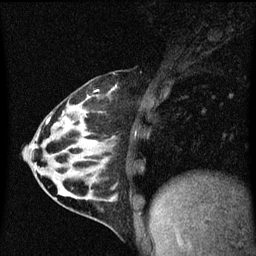
Breast MRI (dynamic contrast-enhanced), one sagittal slice. Dynamic contrast-enhanced series, image 2 of 3 at this slice position (ordered by acquisition). 1.5 T. TE 4.2 ms, TR 8.4 ms. 256 × 256 image matrix, field of view 200 × 200 mm. Patient: female, 32 years.
Structures marked on this image (semi-automatically segmented with operator editing):
- analysis volume of interest (the breast-tissue region the enhancement analysis was run in; not a lesion): bounding box [x1, y1, x2, y2] px = [34, 74, 146, 169]
- tumour enhancement mask (voxels above the 70 % enhancement threshold inside the analysis volume of interest): [47, 86, 118, 123]